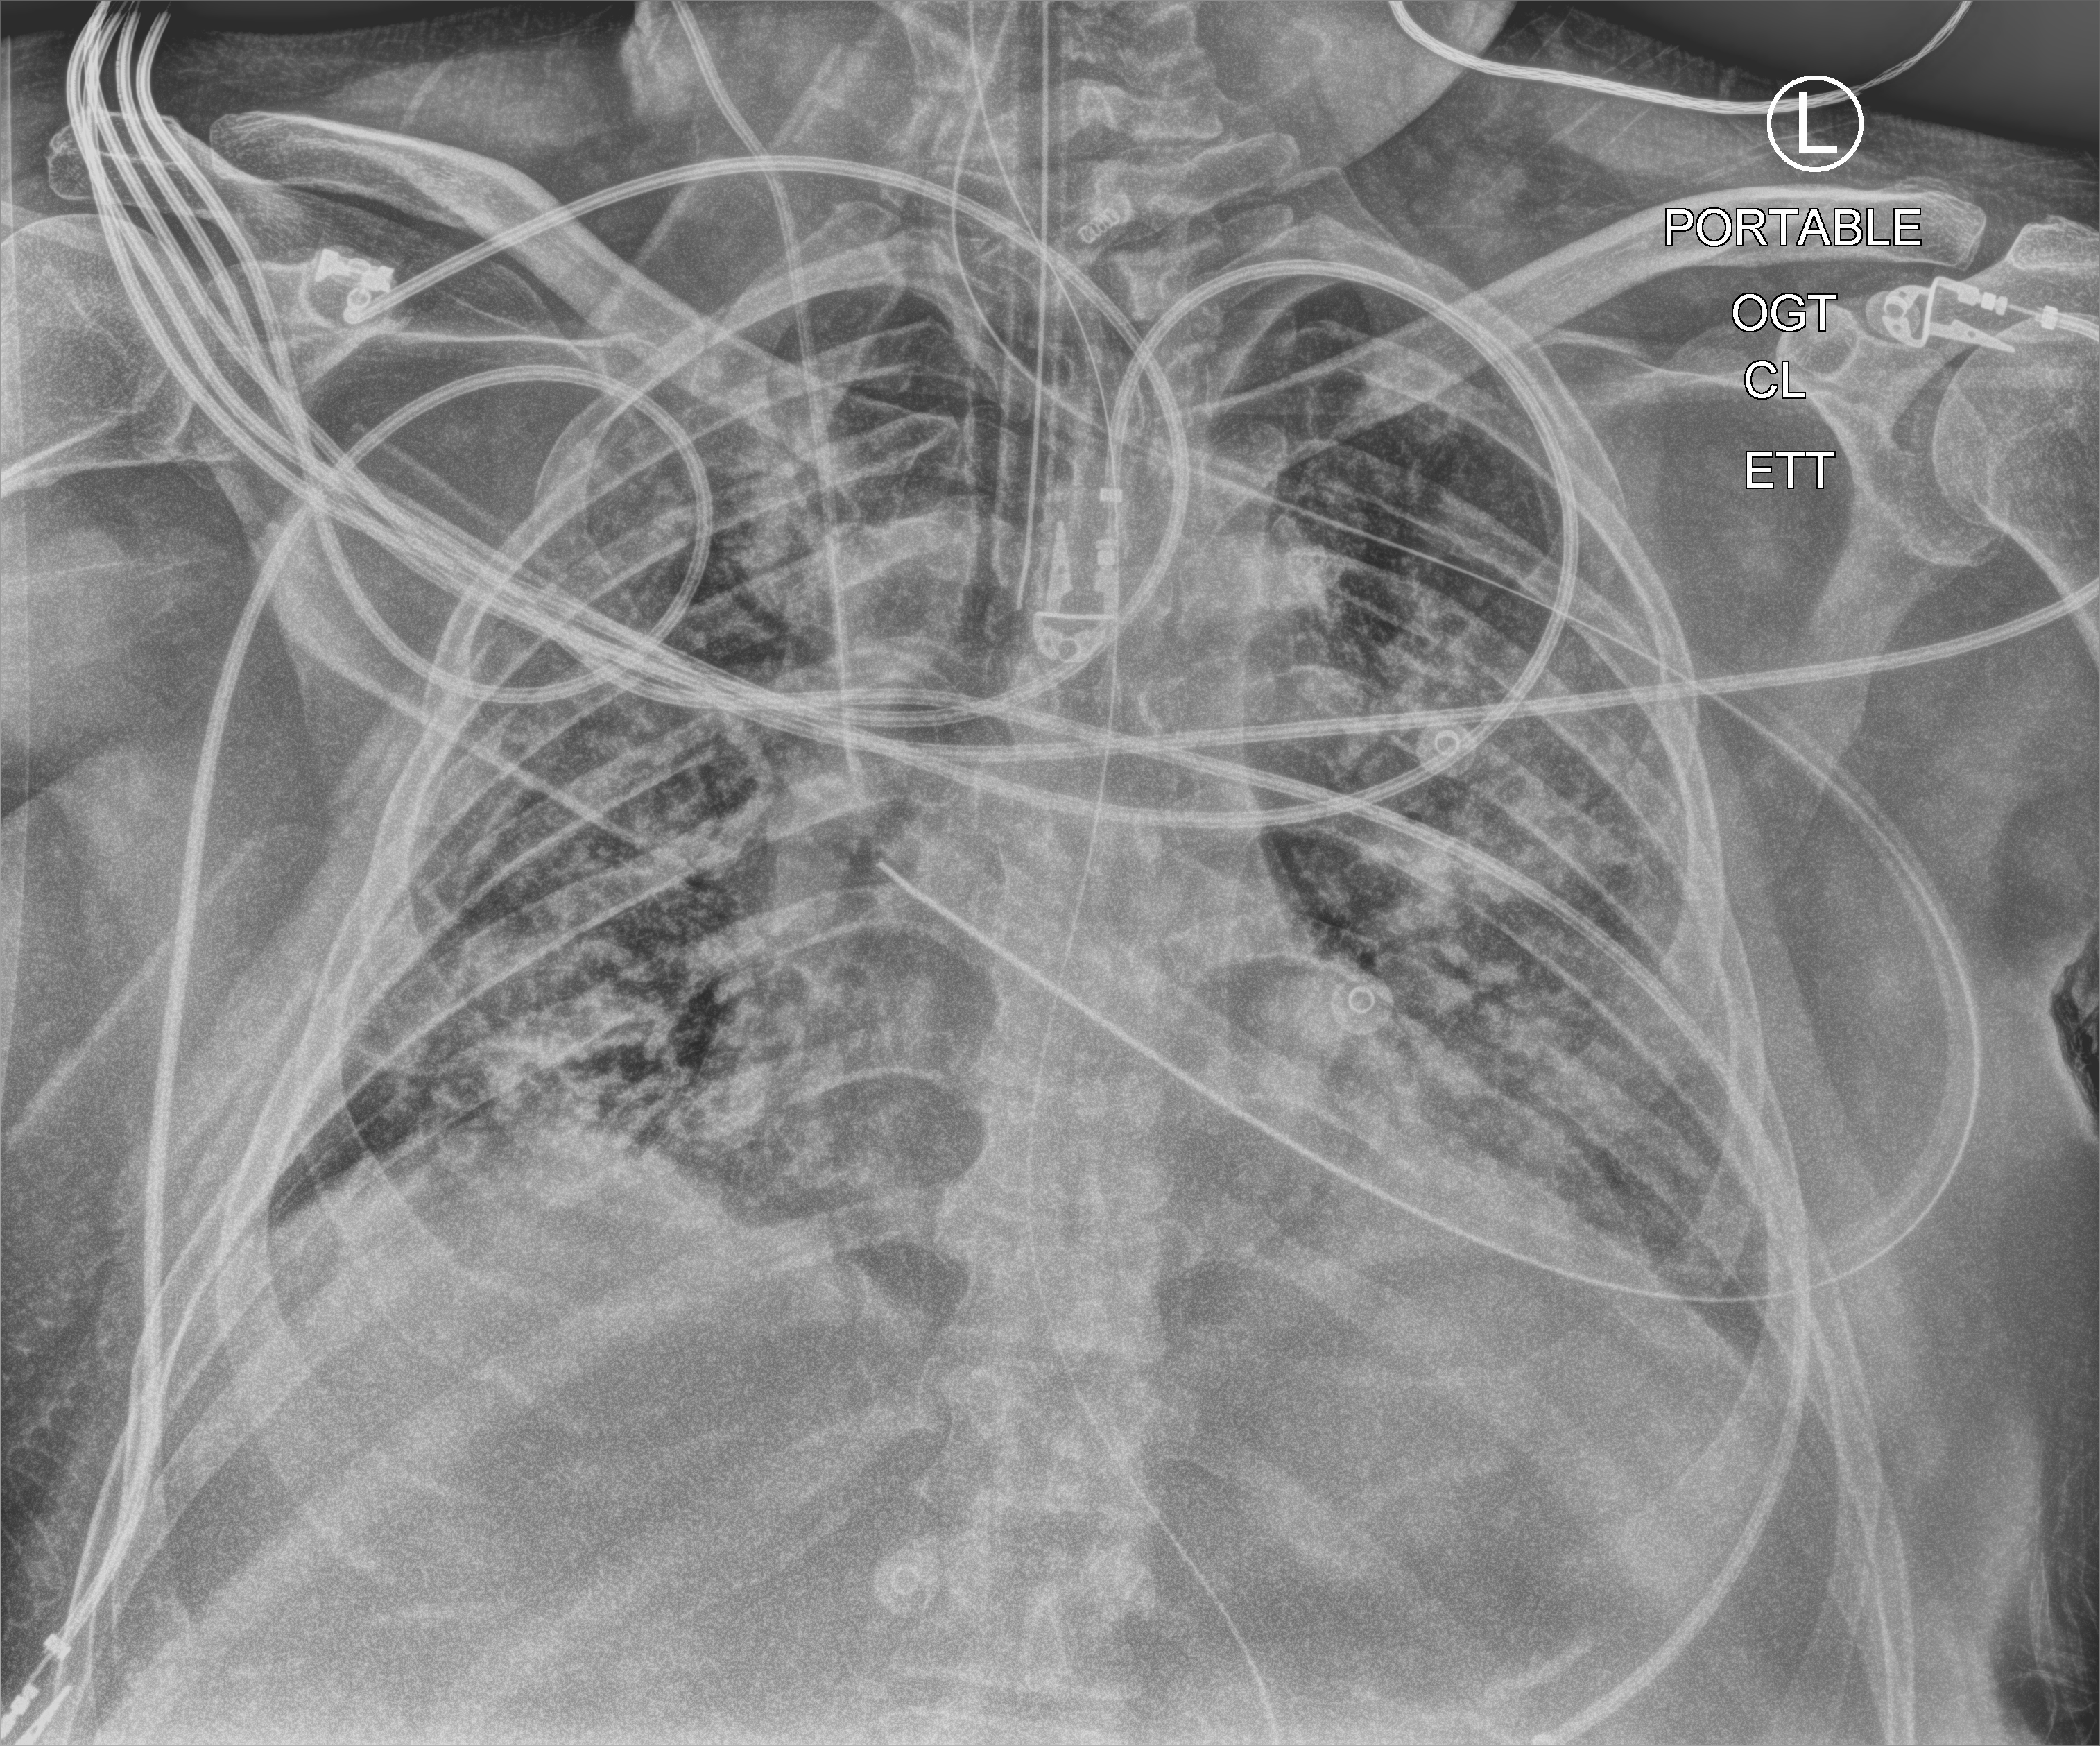
Portable chest radiograph; anteroposterior (AP) projection. Patient hospitalised with COVID-19; male, aged 18–59 years.
From the hospital-stay record, not from the radiograph (when in the stay this image was taken is not recorded): admitted to intensive care during this hospital stay: yes; COPD (admission record): no; mechanically ventilated during this hospital stay: yes.